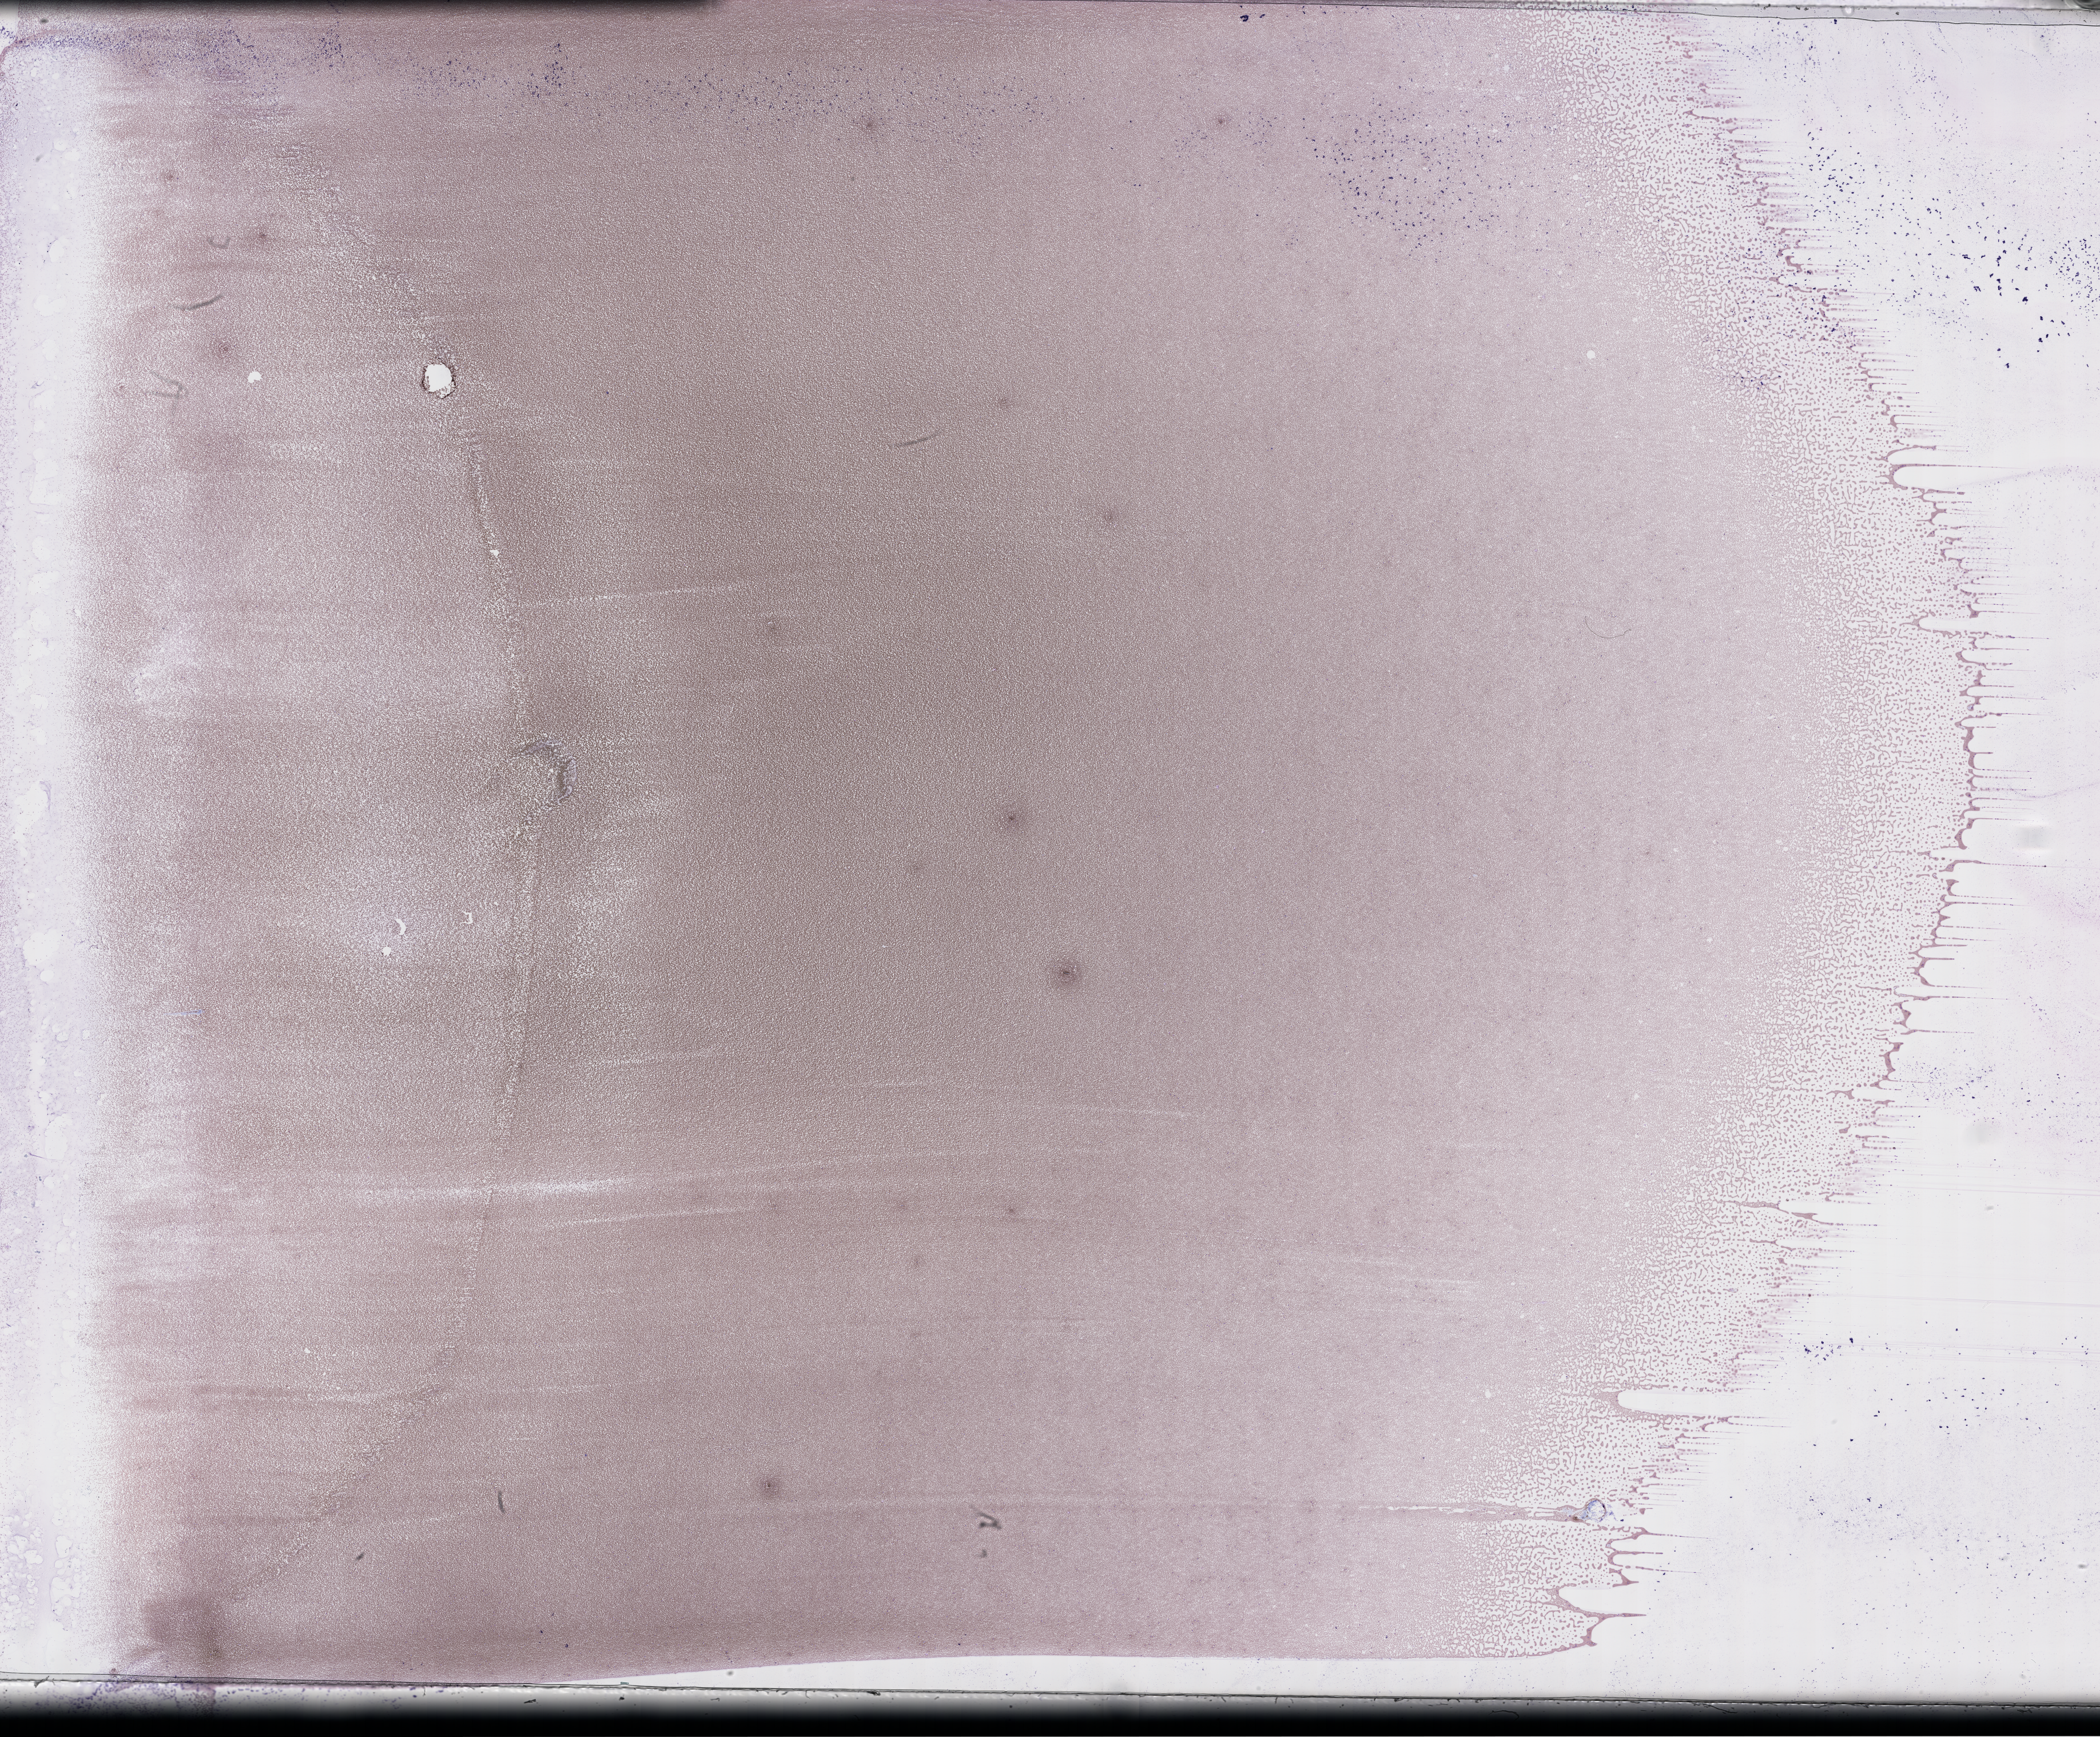
Wright-Giemsa-stained whole blood smear, whole-slide image — shown as a low-resolution overview of the whole scanned area (about 29.7 x 24.5 mm), EDTA-anticoagulated smear, collected at baseline (before treatment). Male patient.
* from a patient with: Plasma Cell Myeloma